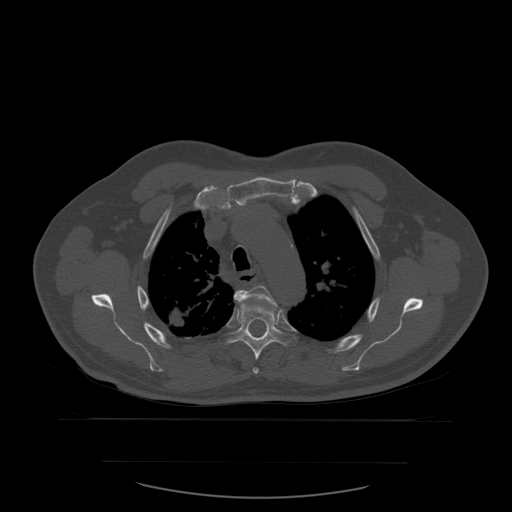
CT including the spine, one axial slice; position 428 of 590 along the scan axis; bone window (W 1800 / L 400 HU); 1.25 mm slice thickness; 512 × 512 image matrix, field of view 479 × 479 mm. Patient age 71 years. Case-level facts recorded for this patient, not image findings: primary cancer: lung; vertebrae with lytic lesions (as recorded): T1, T2, L5, S1.
Outlined on this slice (semi-automatically segmented with operator editing):
- T4 vertebra: box from (x=237, y=286) to (x=278, y=374) px
- T5 vertebra: (x=218, y=292)–(x=298, y=361)